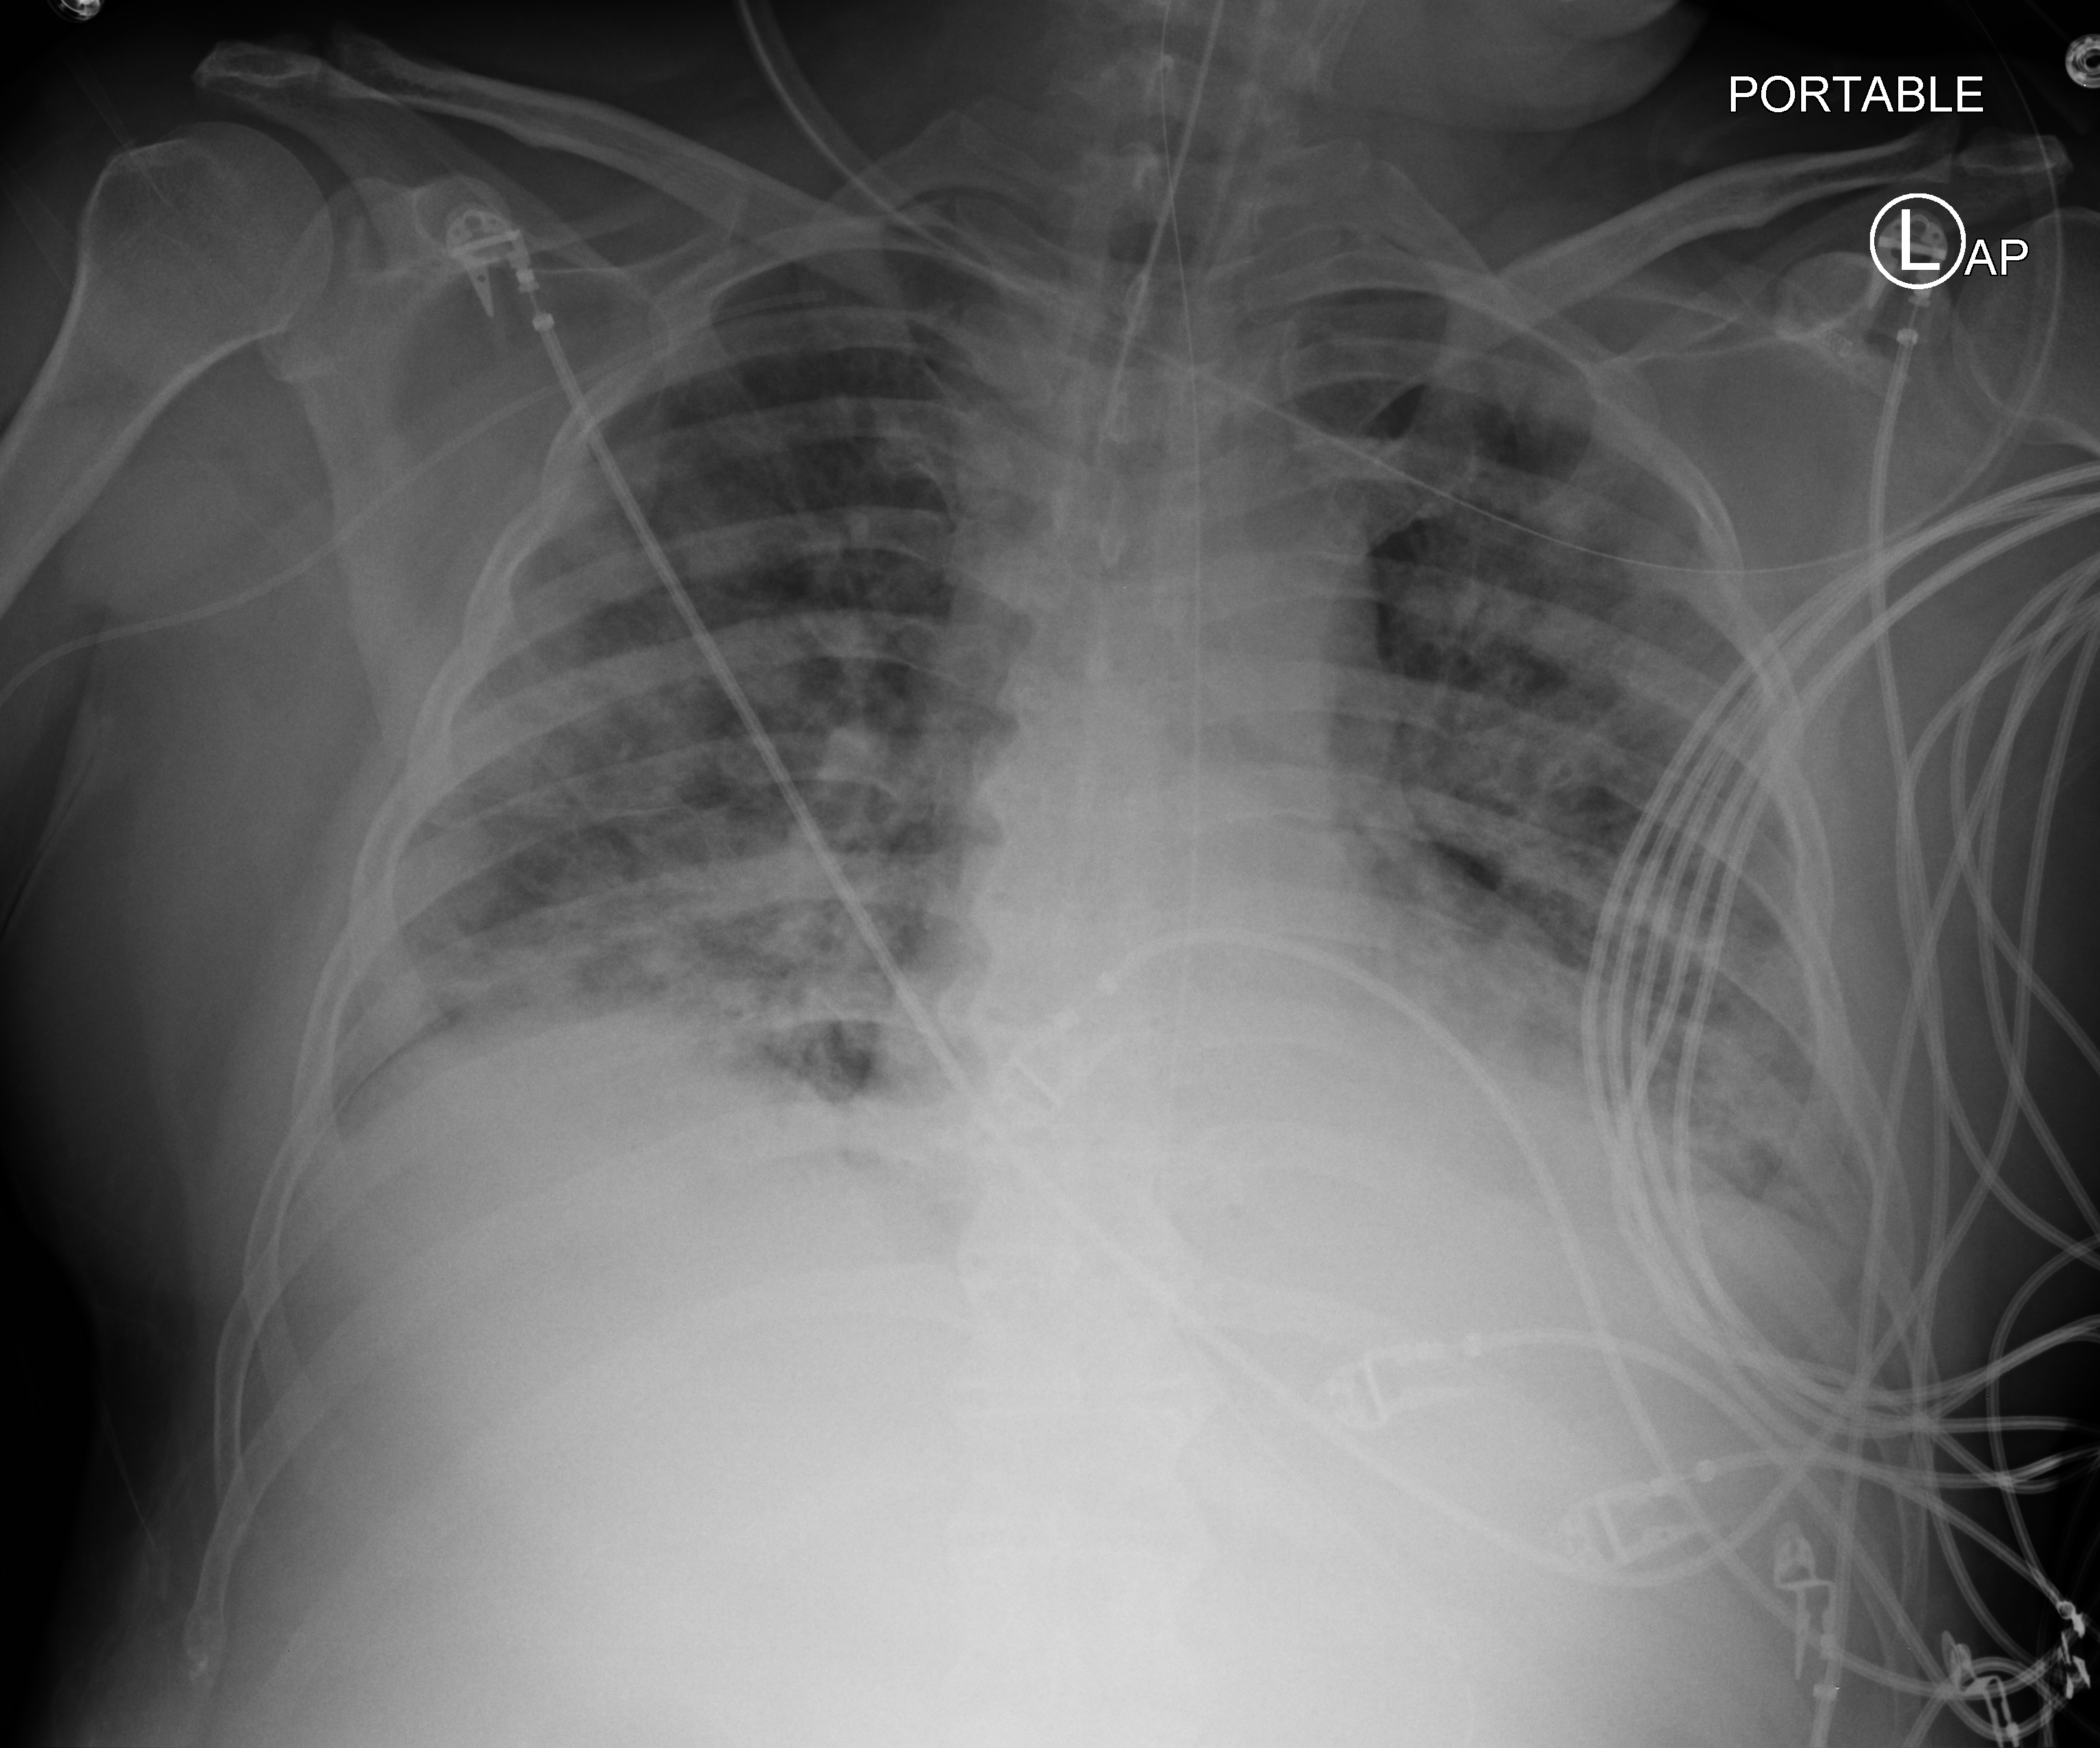
Bedside chest radiograph (computed radiography). Male patient hospitalised with COVID-19, age 18–59 years.
Admission-level facts for this patient (not findings on this image; timing relative to this image not recorded):
- mechanically ventilated during this hospital stay: yes
- admitted to intensive care during this hospital stay: yes